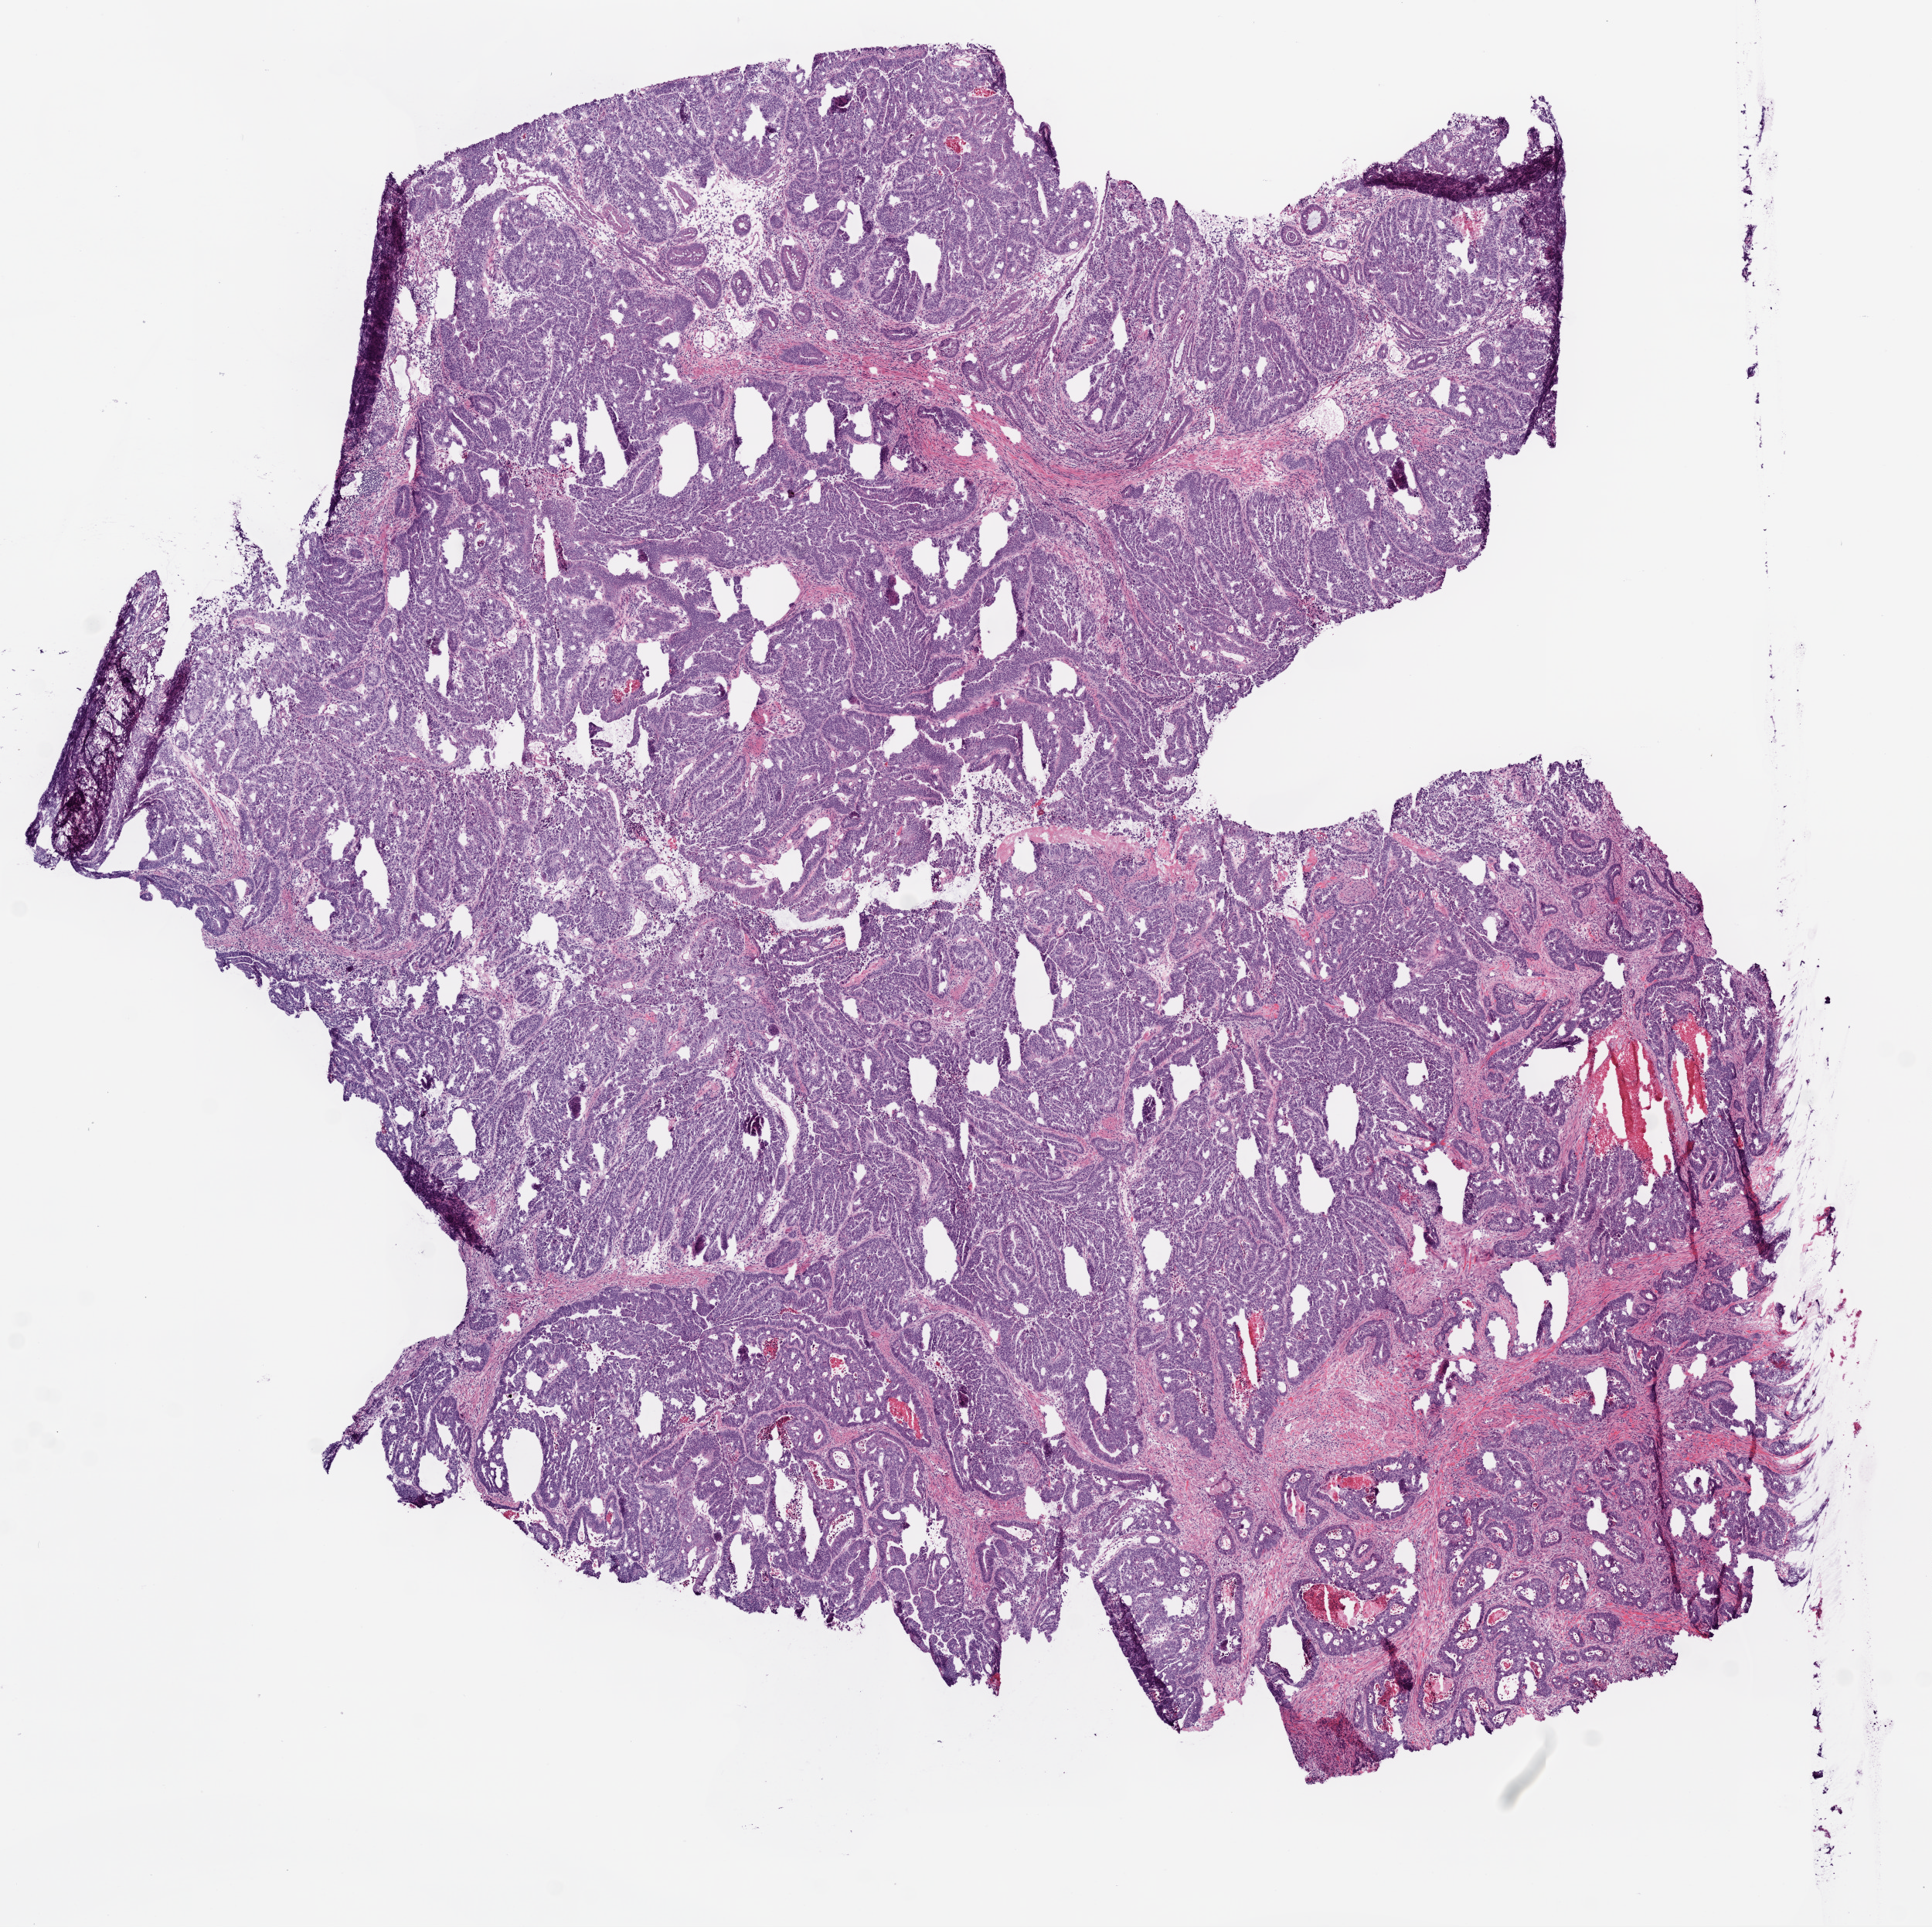
Digitized H&E-stained tissue section (whole slide) — shown as a low-resolution overview of the whole scanned area (about 10.0 x 10.0 mm, from a 20x scan), frozen section, primary tumour sample from the rectum. Female, age 85 years at initial diagnosis. Composition of this section per pathologist review: tumour cells 77%, tumour nuclei 80%, normal cells 15%, stromal cells 5%, necrosis 3%.
• TNM: T3 N0 M0
• pathologic diagnosis: Adenocarcinoma, NOS (colon, NOS)
• lymph nodes positive (case pathology): 0 of 24 examined
• AJCC pathologic stage: IIA (6th edition)